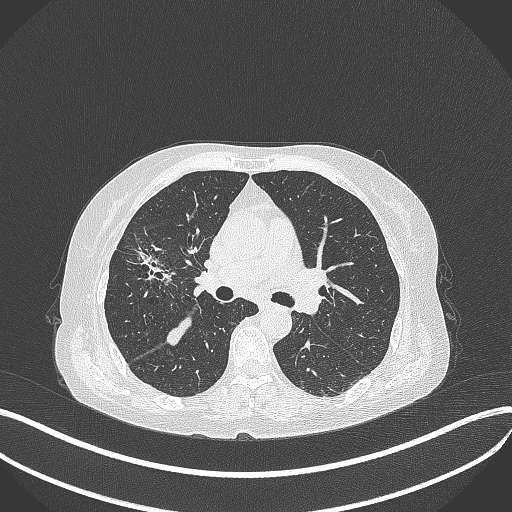
Chest CT, one axial slice. Position 236 of 429 along the scan axis. Lung window (W 1500 / L -600 HU). 1 mm slice thickness. 512 × 512 image matrix, field of view 400 × 400 mm. Female patient, age 69 years. From the clinical record (not read from this slice): clinical TNM (as recorded): T1b N3 M0.
Structures marked on this image (rectangle marked by the reading radiologist):
- lung tumour (recorded histology: small cell carcinoma): bounding box (x1, y1, x2, y2) in pixels: (121, 231, 179, 287)